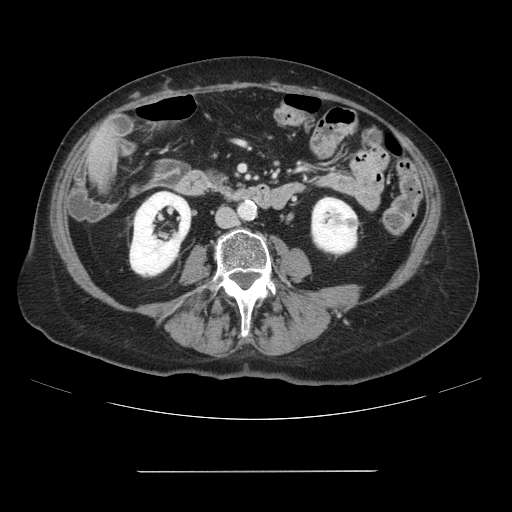
Contrast-enhanced abdominal CT, one axial slice. Position 7 of 111 along the scan axis. 120 kVp. Soft-tissue window (W 400 / L 40 HU). 2.5 mm slice thickness. 512 × 512 image matrix, field of view 400 × 400 mm. Female patient, age 74 years. Case-level facts recorded for this patient, not image findings: diagnosis: colorectal cancer liver metastases, imaged before liver resection; multiple liver metastases: yes; largest metastasis: 1.1 cm; chemotherapy before resection: yes.
Annotated regions visible in this slice (manually delineated by an expert):
- liver: bounding box <89,124,117,182> (left, top, right, bottom; pixels)